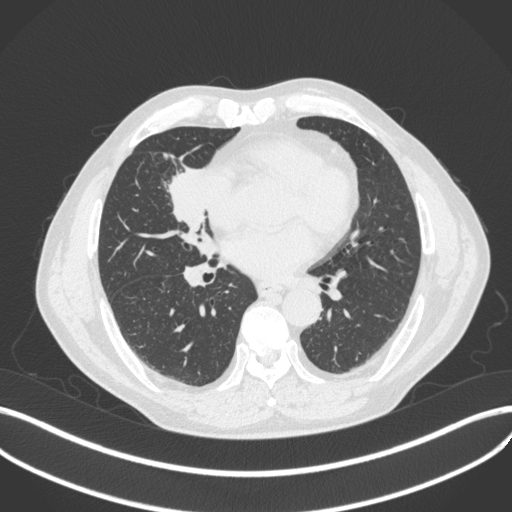
Chest CT, one axial slice; position 184 of 429 along the scan axis; 120 kVp; lung window (W 1500 / L -600 HU); 512 × 512 image matrix, field of view 400 × 400 mm. Patient: male, 61 years. Case-level facts recorded for this patient, not image findings: clinical TNM (as recorded): T2b N1 M0.
Outlined on this slice (rectangle marked by the reading radiologist):
- lung tumour (recorded histology: squamous cell carcinoma): bounding box [x1, y1, x2, y2] px = [165, 157, 218, 237]